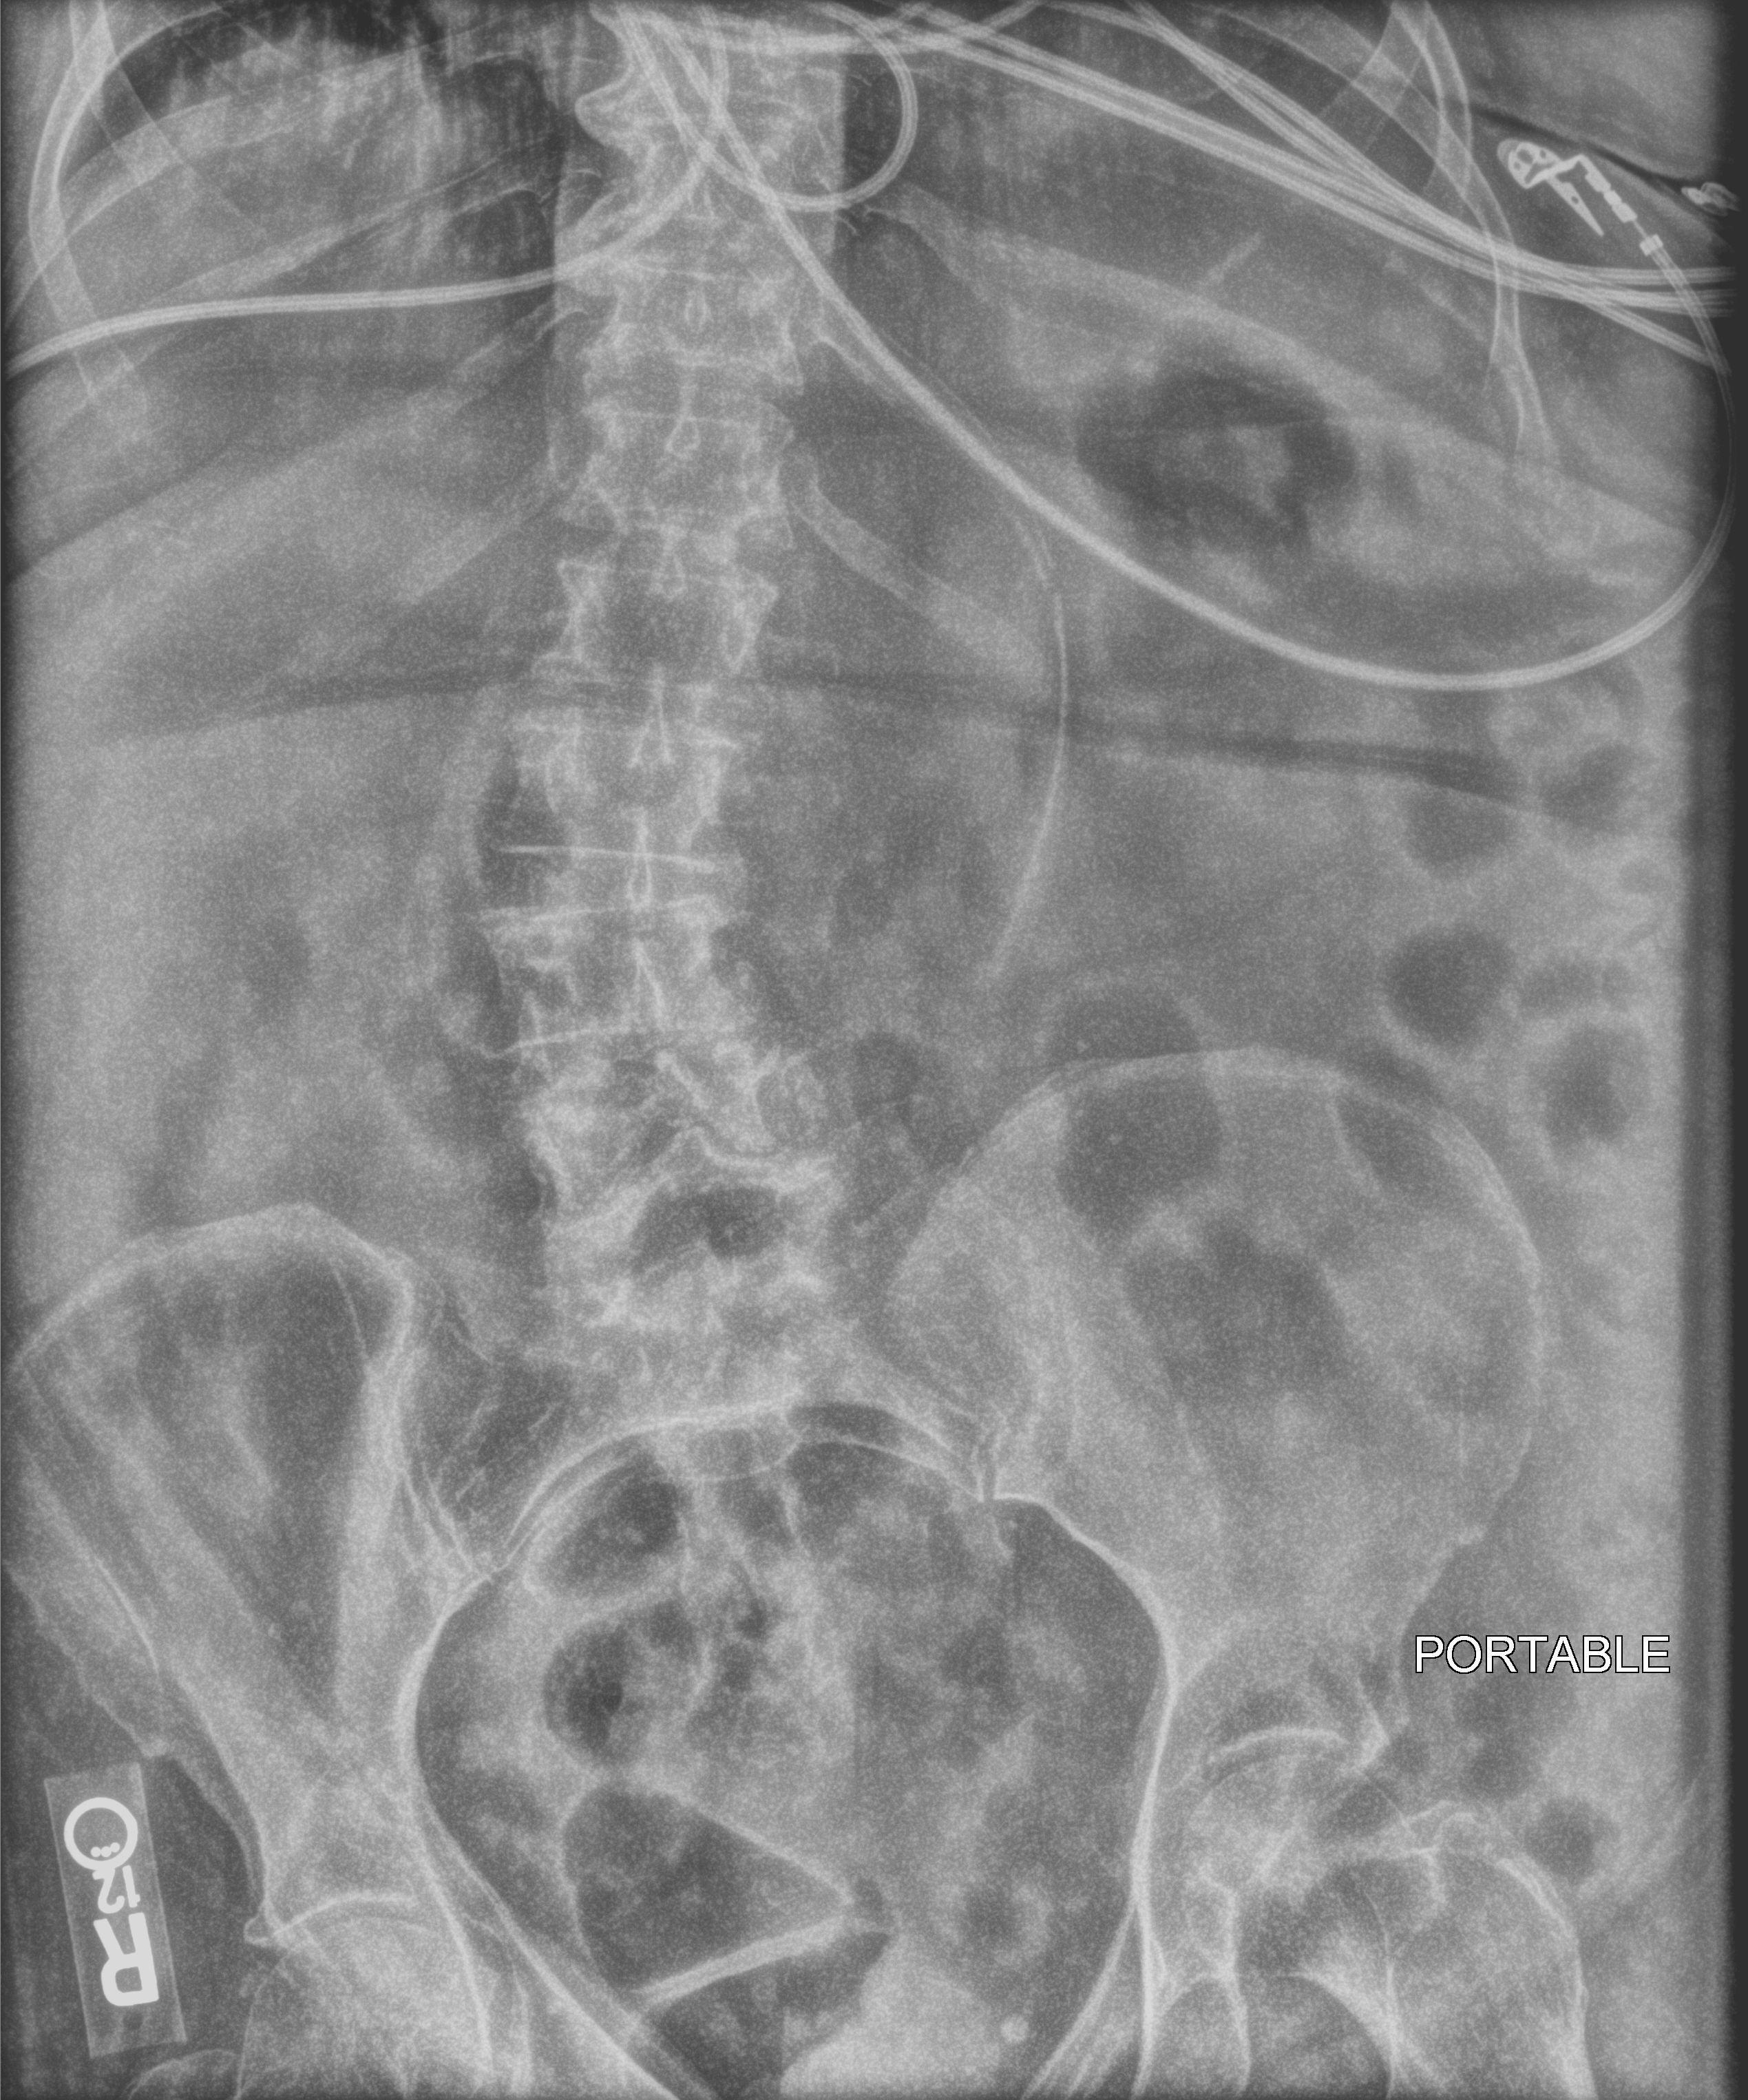
Bedside abdomen radiograph (computed radiography); anteroposterior (AP) projection. Female patient hospitalised with COVID-19, age 75–90 years.
Admission-level facts for this patient (not findings on this image; timing relative to this image not recorded): chronic kidney disease (admission record): no; diabetes (admission record): no; smoking status (admission record): former.